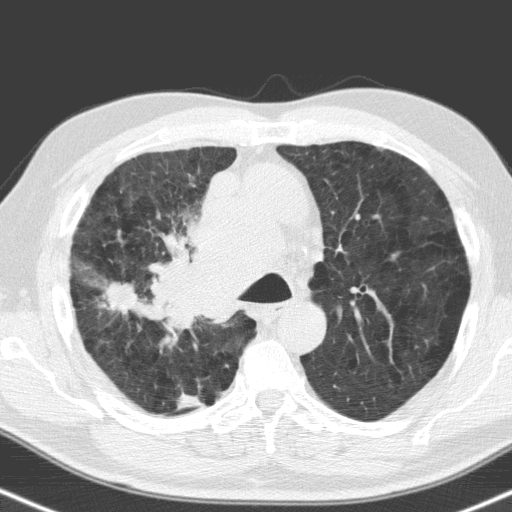
Low-dose screening chest CT, axial slice. Baseline annual screen. Lung window (W 1500 / L -600 HU). Standard (soft-tissue) reconstruction kernel (C). Slice 47 of 160 in the series. 512 × 512 image matrix. Male participant, aged 71 years at enrolment. Former smoker at enrolment.
Expert reader's lesion annotation, bounding box <90,272,166,338> (left, top, right, bottom; pixels). The screening reader recorded 2 non-calcified nodules or masses ≥4 mm on this exam; which of them this box marks is not recorded. Later outcome: lung cancer diagnosed 31 days after this screen — small cell carcinoma, NOS, right upper lobe, stage IV (AJCC 6th edition), 40 mm at pathology.